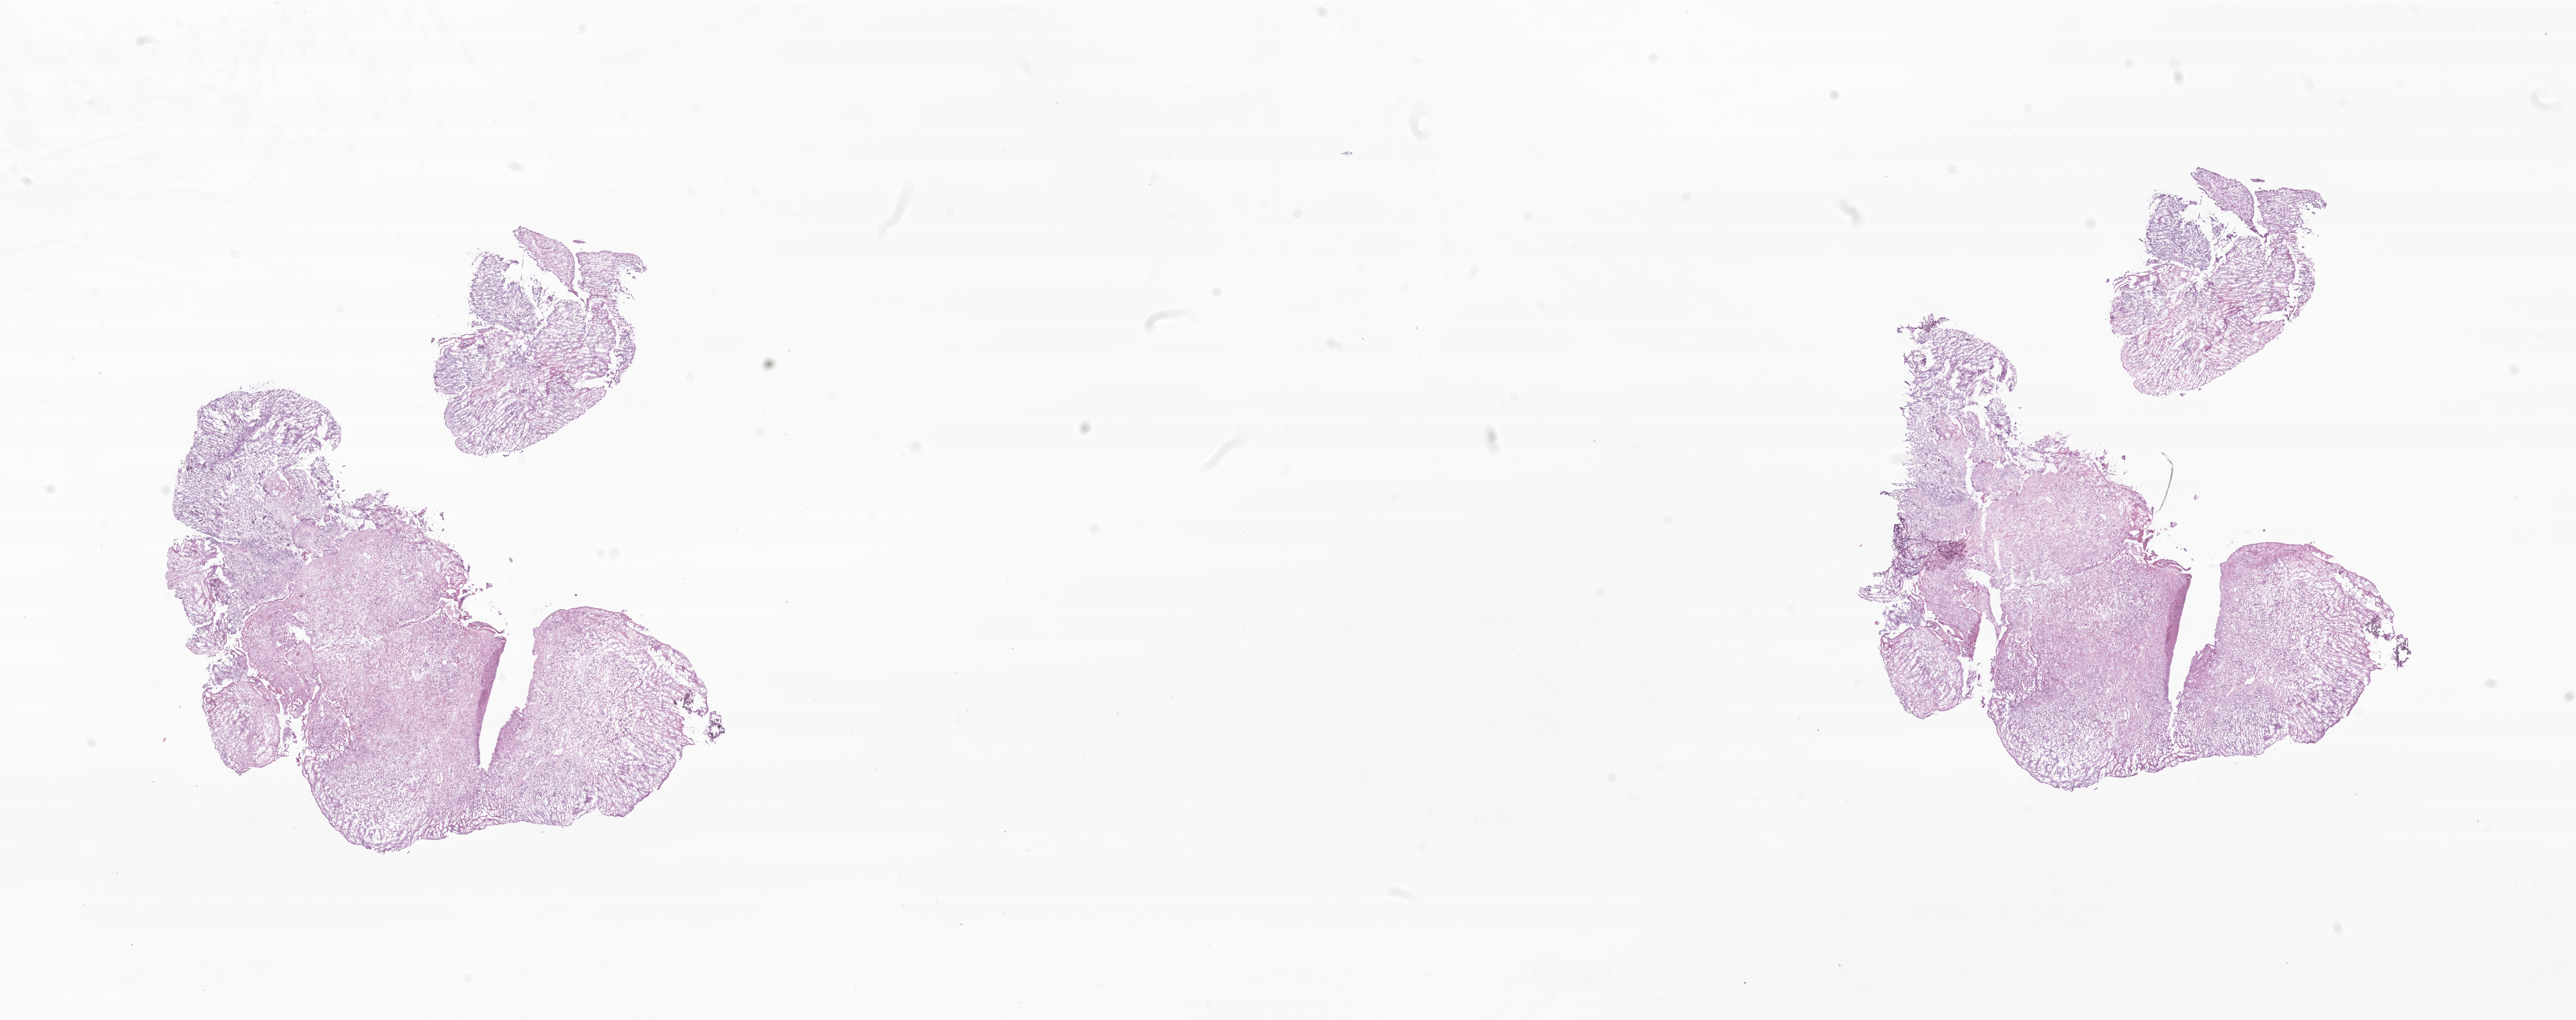
Digitized H&E-stained section of tumor tissue from the brain — a low-resolution overview of the entire scanned area, about 28.7 x 11.4 mm. Frozen section (OCT-embedded). Patient female; age 162 months (13 years 6 months).
Diagnosis (ICD-O-3 morphology term): Ependymoma, NOS.